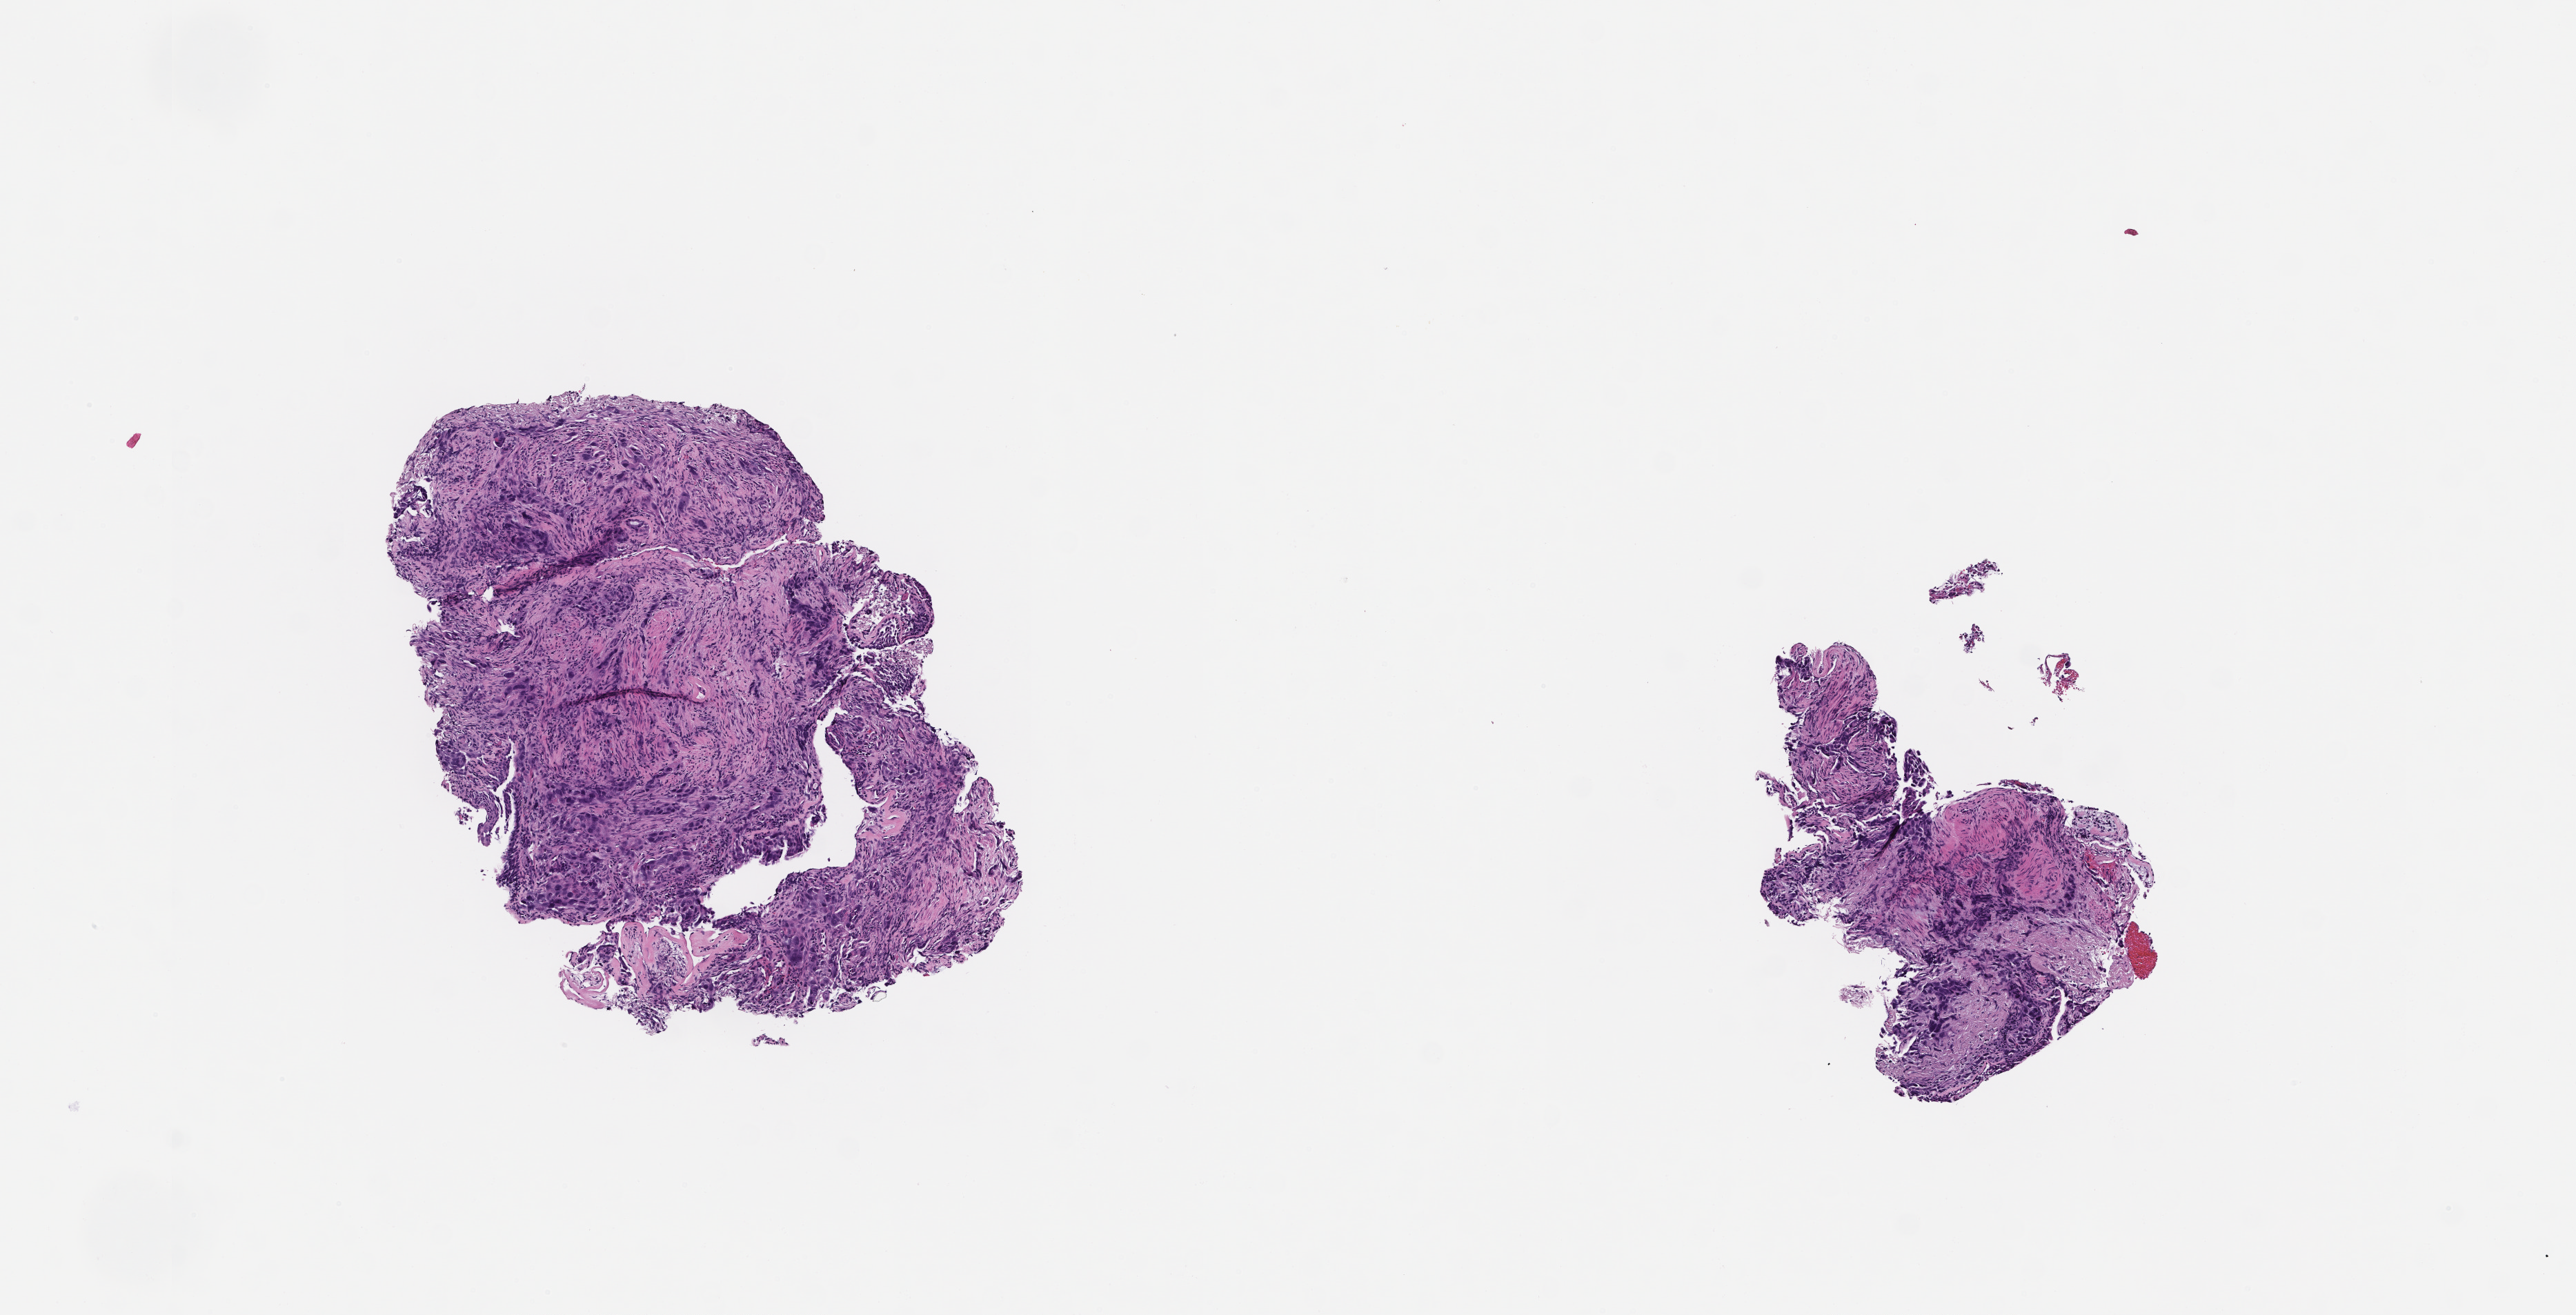
H&E whole-slide image — whole scanned area (about 7.5 x 3.8 mm) shown as a low-resolution overview. Formalin-fixed paraffin-embedded section. Tissue site: lung. Specimen time point: collected at baseline (before treatment). Patient sex: male.
This section: primary tumor. Diagnosis: Non-Small Cell Lung Carcinoma.